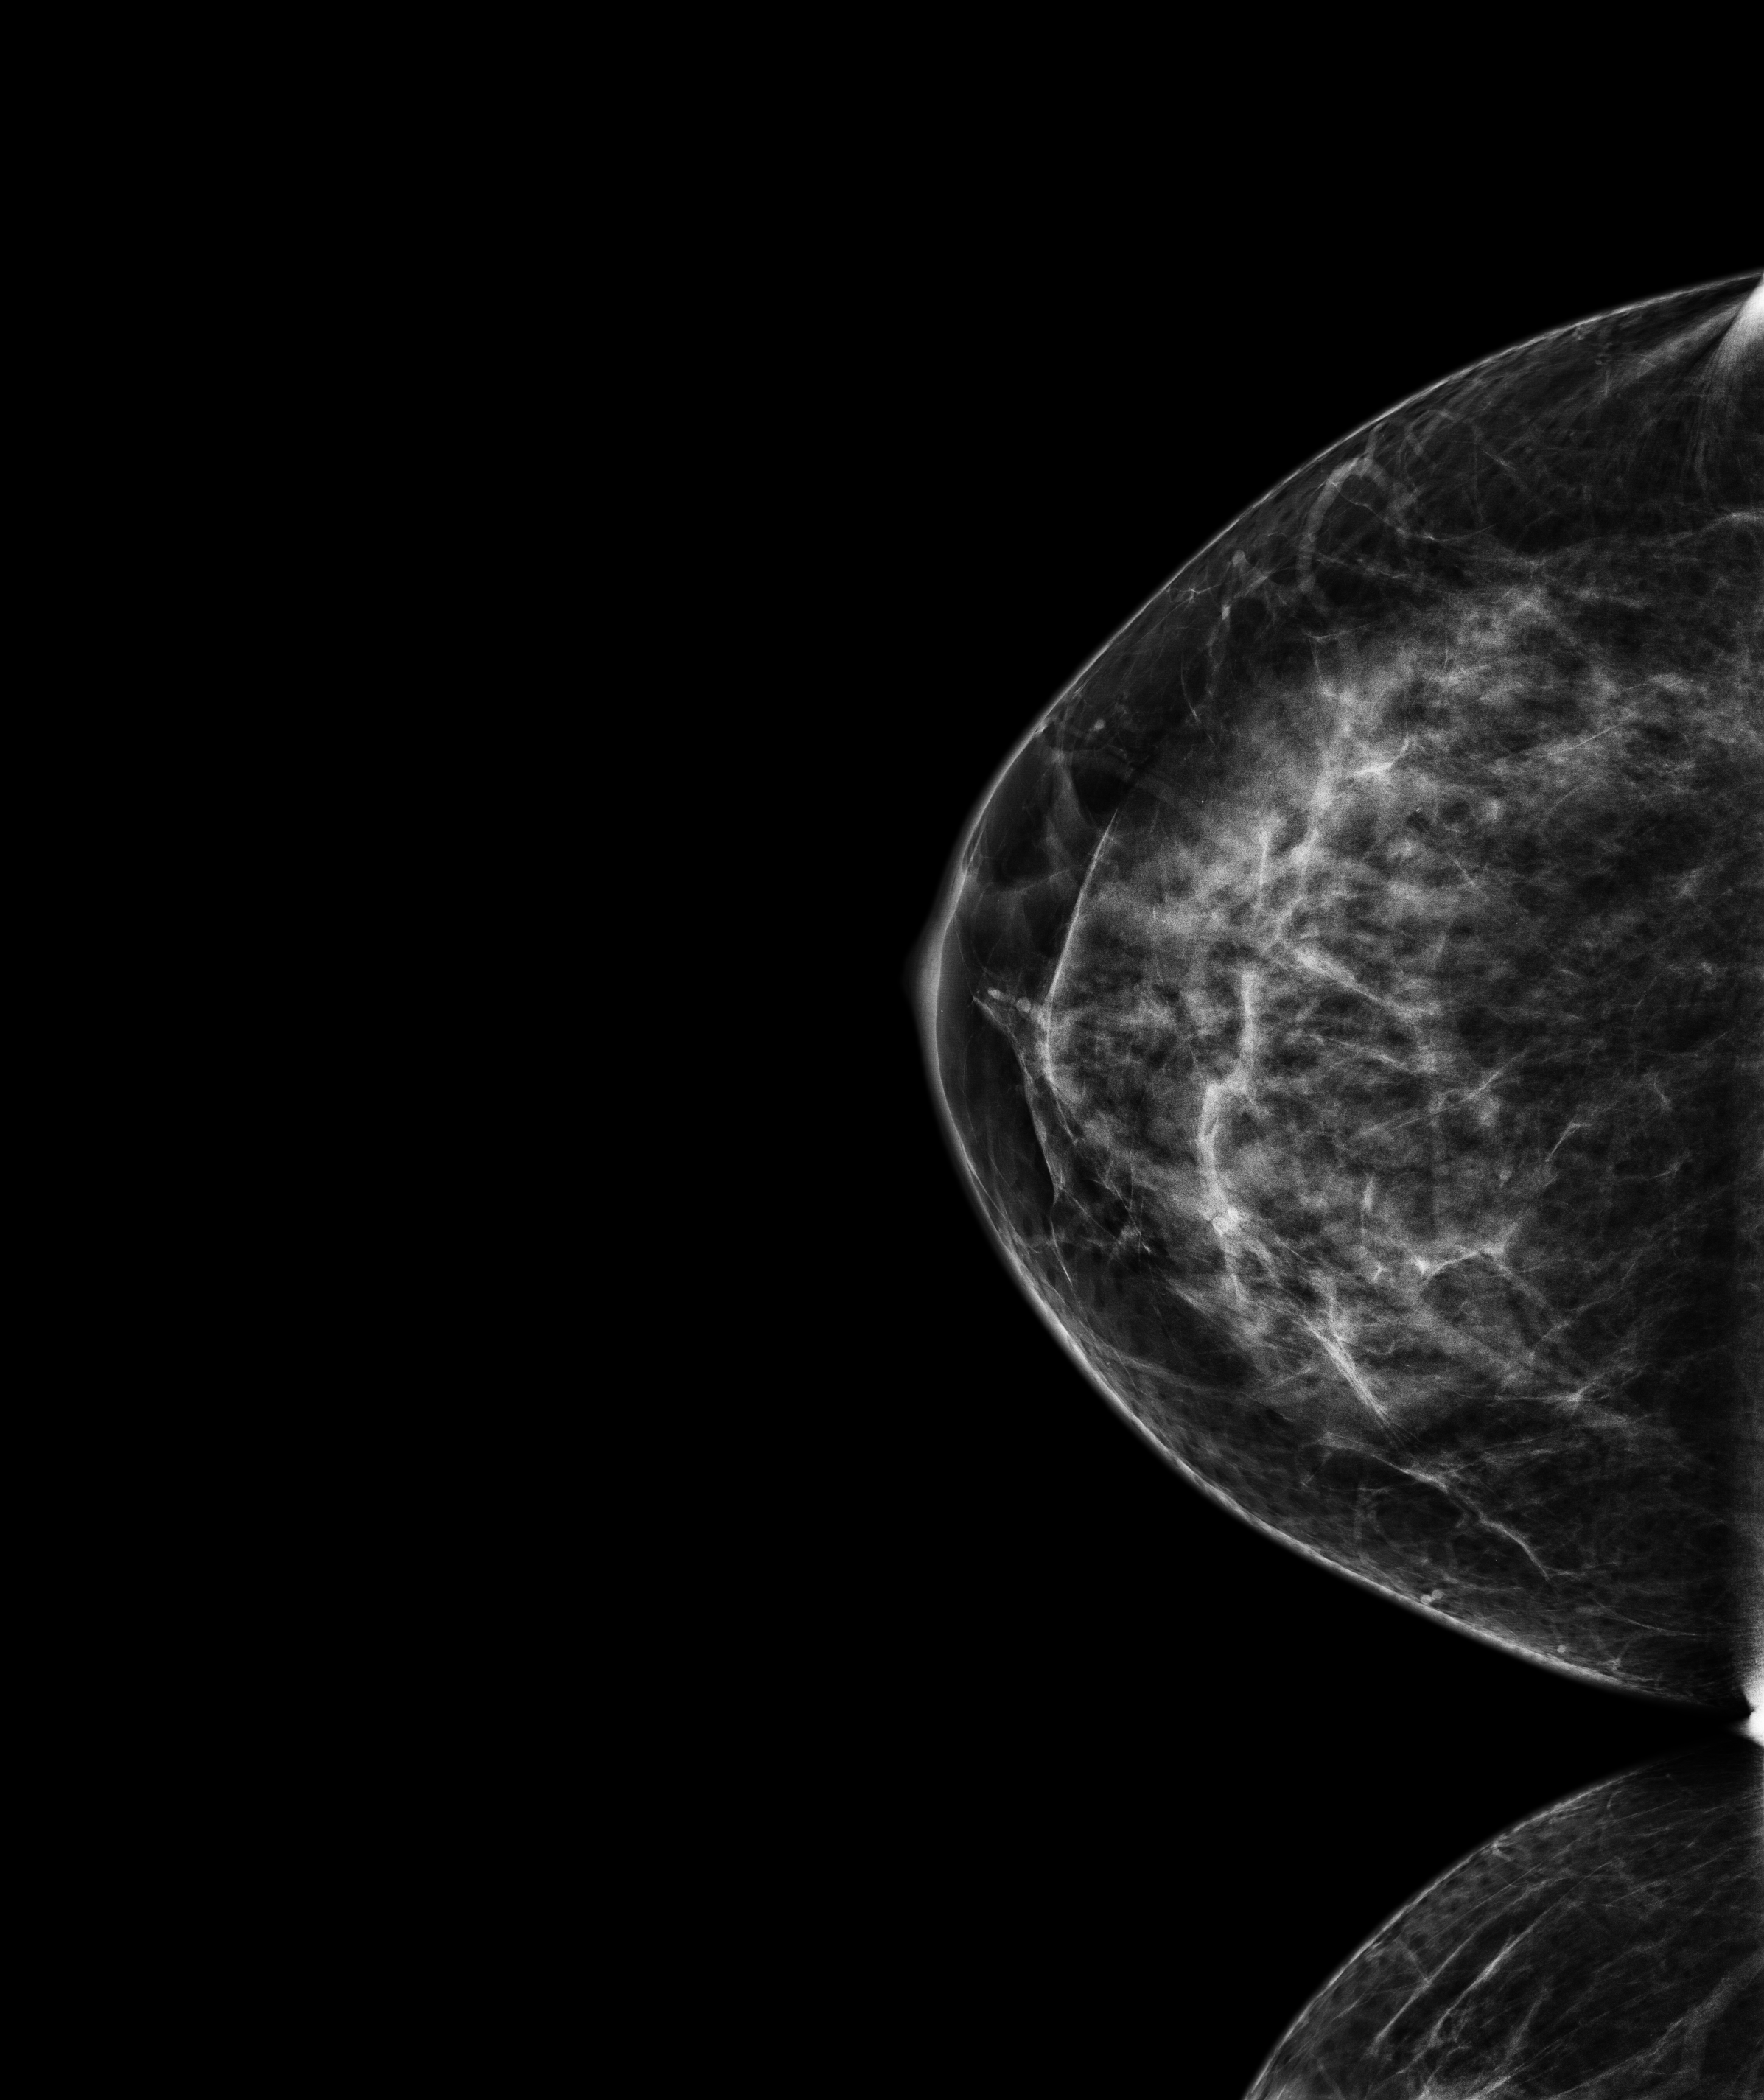
Screening examination, compressed breast thickness 69.6 mm, system: Senographe Pristina. Patient aged 45 years (female).
Image type: full-field digital mammogram. Breast: right. Projection: craniocaudal (CC) view.